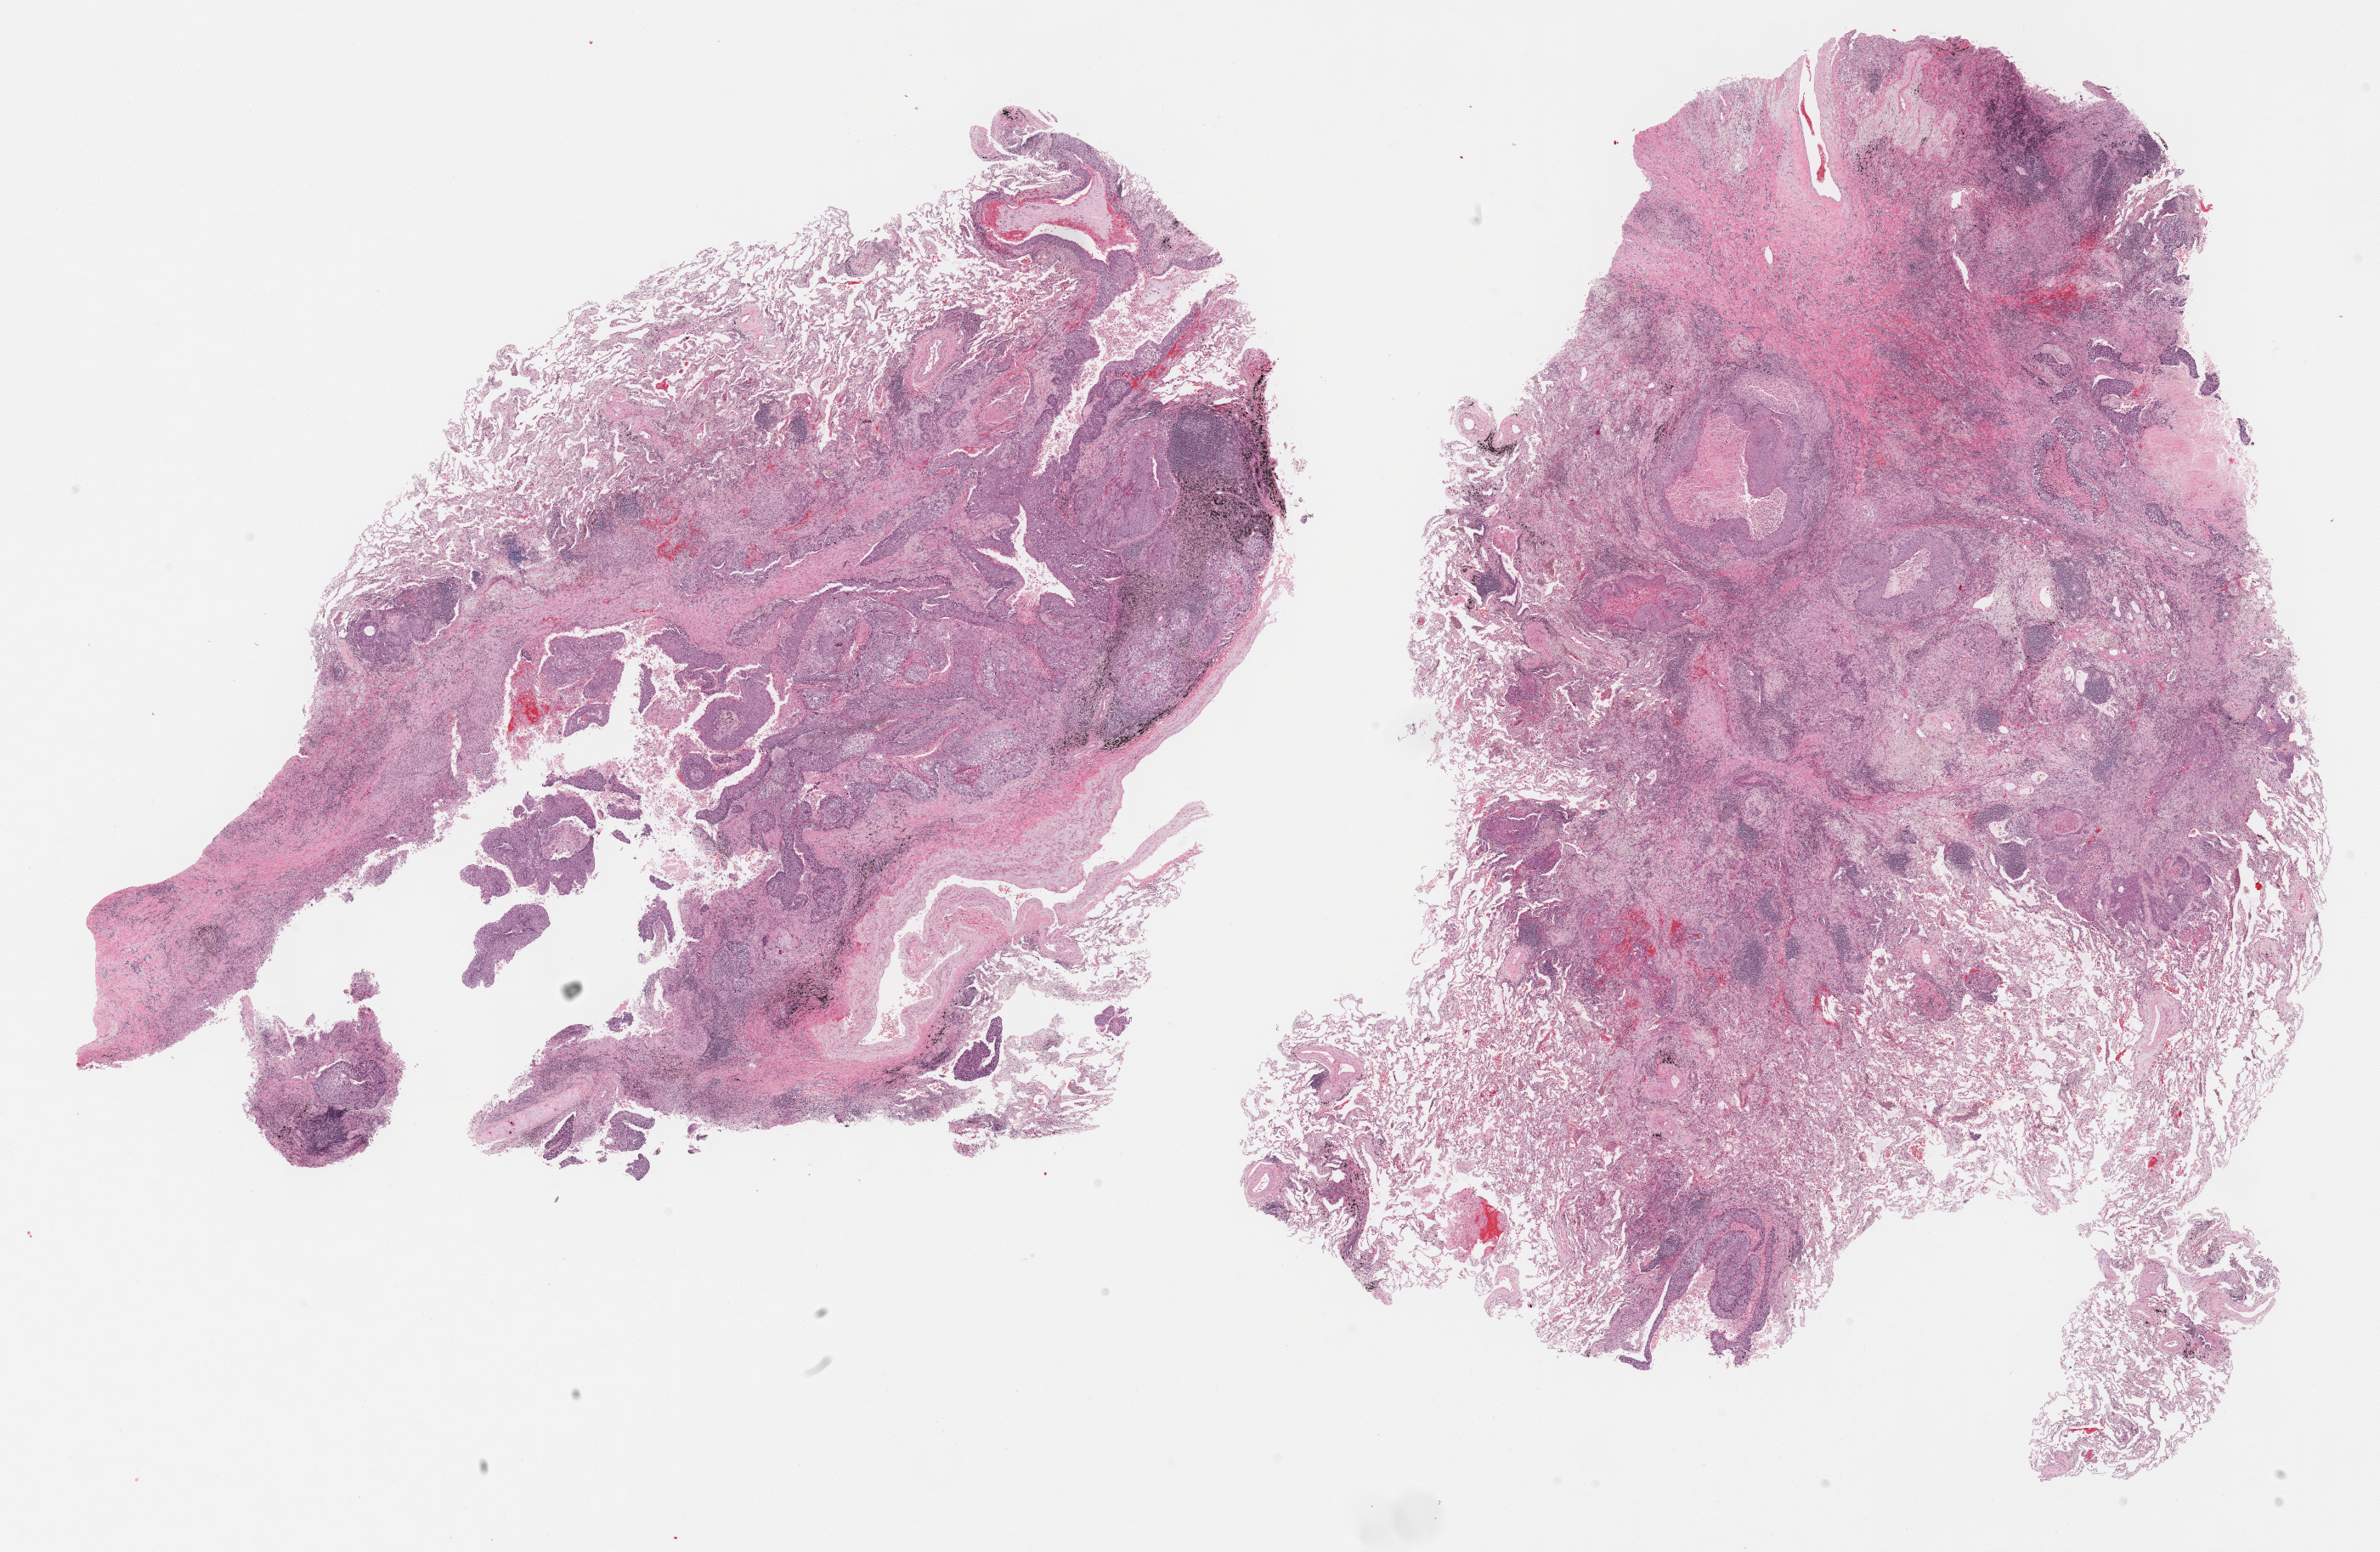
Whole-slide histology image, H&E — shown as a low-resolution overview of the whole scanned area (about 22.7 x 14.8 mm), FFPE section, primary tumour sample from the lung. Patient: female, age at initial diagnosis 77 years.
AJCC pathologic stage: IA (7th edition). TNM: T1a N0 M0. Histologic diagnosis: Squamous cell carcinoma, NOS (lower lobe, lung).